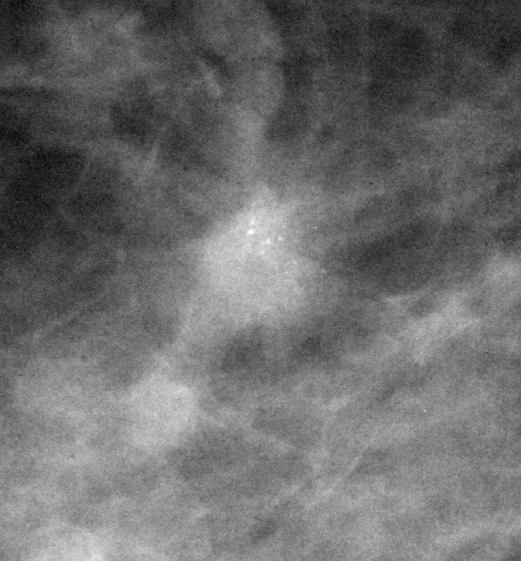
Crop from a digitized film mammogram around one marked abnormality; right breast; MLO view; BI-RADS breast density category 2 (scale 1–4).
Finding: calcifications, morphology pleomorphic, distribution clustered; BI-RADS assessment category 5; subtlety rating 5 on a 1 (subtle) to 5 (obvious) scale; pathology (as recorded): malignant.